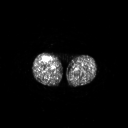
FDG PET of an extremity soft-tissue mass (from a PET/CT study), one axial slice; position 255 of 311 along the scan axis; 3.27 mm slice thickness; 128 × 128 image matrix, field of view 700 × 700 mm. Patient: male, 56 years. From the clinical record (not read from this slice): histological type: pleiomorphic leiomyosarcoma; grade: intermediate; site of the primary tumour: right thigh.
Annotated regions visible in this slice (expert contour drawn on MRI and transferred to this co-registered scan by the dataset authors):
- gross tumour volume including surrounding oedema: box from (x=43, y=56) to (x=51, y=62) px